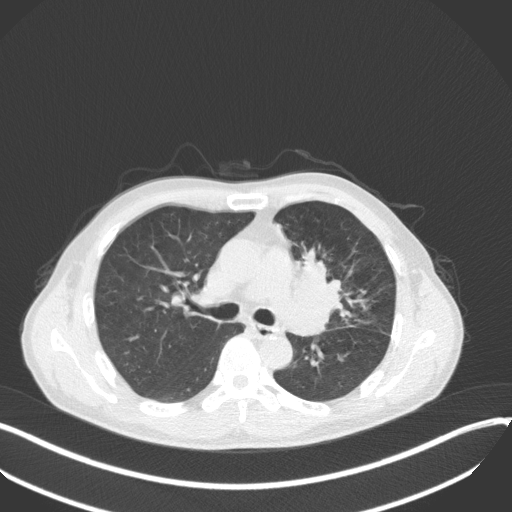
Chest CT, one axial slice. Slice 209 of 411 in the series (ordered by position). Lung window (W 1500 / L -600 HU). 1 mm slice thickness. 512 × 512 image matrix, field of view 400 × 400 mm. Patient: male, 56 years. Case-level facts recorded for this patient, not image findings: clinical TNM (as recorded): T2a N0 M0.
Annotated regions visible in this slice (bounding box drawn by a radiologist):
- lung tumour (recorded histology: squamous cell carcinoma): bounding box <290,237,345,334> (left, top, right, bottom; pixels)